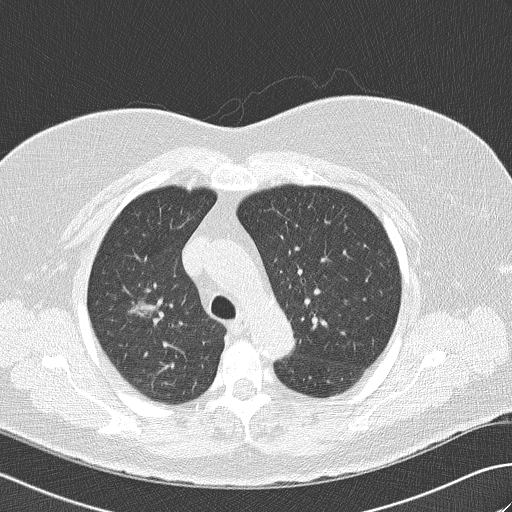
Low-dose screening chest CT, axial slice. Second annual screen. Lung window (W 1500 / L -600 HU). 2 mm slice thickness. 120 kVp. Slice 113 of 148 in the series. Female, age 74 years at enrolment. Former smoker at enrolment.
Expert-annotated lung lesion, bounding box [x1, y1, x2, y2] px = [104, 281, 173, 338]. The screening reader recorded 4 non-calcified nodules or masses ≥4 mm on this exam (right upper lobe, right middle lobe, right middle lobe, left lower lobe); which of them this box marks is not recorded. Official screen result: positive, other.